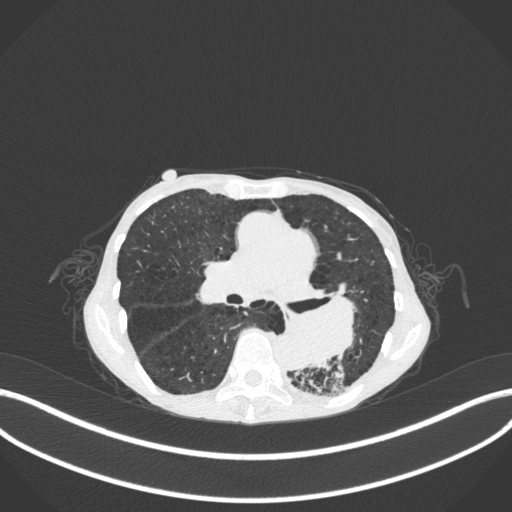
Chest CT, one axial slice; slice 153 of 347 in the series (ordered by position); reconstruction kernel B31f; lung window (W 1500 / L -600 HU); 1 mm slice thickness; 512 × 512 image matrix, field of view 400 × 400 mm. Patient: female, 70 years. Case-level facts recorded for this patient, not image findings: clinical TNM (as recorded): T3 N0 M0.
Annotated regions visible in this slice (rectangle marked by the reading radiologist):
- lung tumour (recorded histology: small cell carcinoma): bounding box (x1, y1, x2, y2) in pixels: (282, 289, 371, 372)